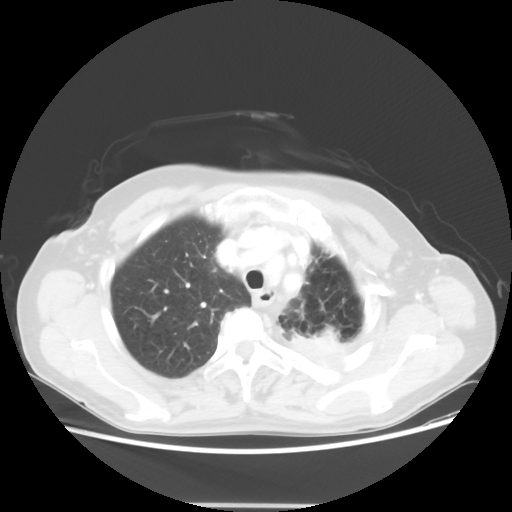
Chest CT, one axial slice; position 43 of 56 along the scan axis; reconstruction kernel STANDARD; lung window (W 1500 / L -600 HU); 512 × 512 image matrix. Patient: female, 63 years. Case-level facts recorded for this patient, not image findings: clinical TNM (as recorded): T2a N0 M0.
Outlined on this slice (bounding box drawn by a radiologist):
- lung tumour (recorded histology: adenocarcinoma): bounding box <290,323,346,356> (left, top, right, bottom; pixels)